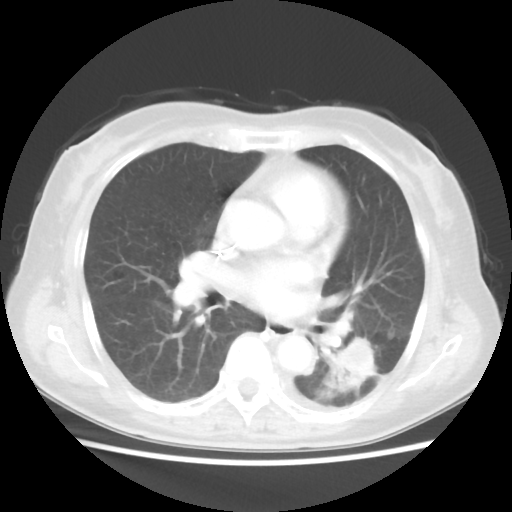
Chest CT, one axial slice. Position 19 of 40 along the scan axis. Lung window (W 1500 / L -600 HU). 5 mm slice thickness. 512 × 512 image matrix, field of view 341 × 341 mm. Female patient, age 69 years. Case-level facts recorded for this patient, not image findings: clinical TNM (as recorded): T1c N0 M0.
Outlined on this slice (bounding box drawn by a radiologist):
- lung tumour (recorded histology: adenocarcinoma): bounding box [x1, y1, x2, y2] px = [334, 335, 378, 393]